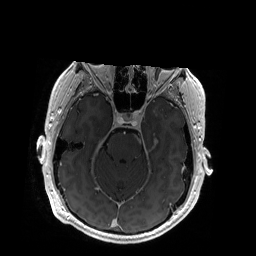
Brain MRI from a brain-tumour surgery series, one axial slice. Position 126 of 192 along the scan axis. T1-weighted post-contrast. 1 mm slice thickness. 256 × 256 image matrix, field of view 256 × 256 mm. Case-level facts recorded for this patient, not image findings: histopathology: Glioblastoma; WHO grade: 4; IDH mutation: no.
Outlined on this slice (manually delineated by an expert):
- tumour: box from (x=137, y=137) to (x=158, y=144) px